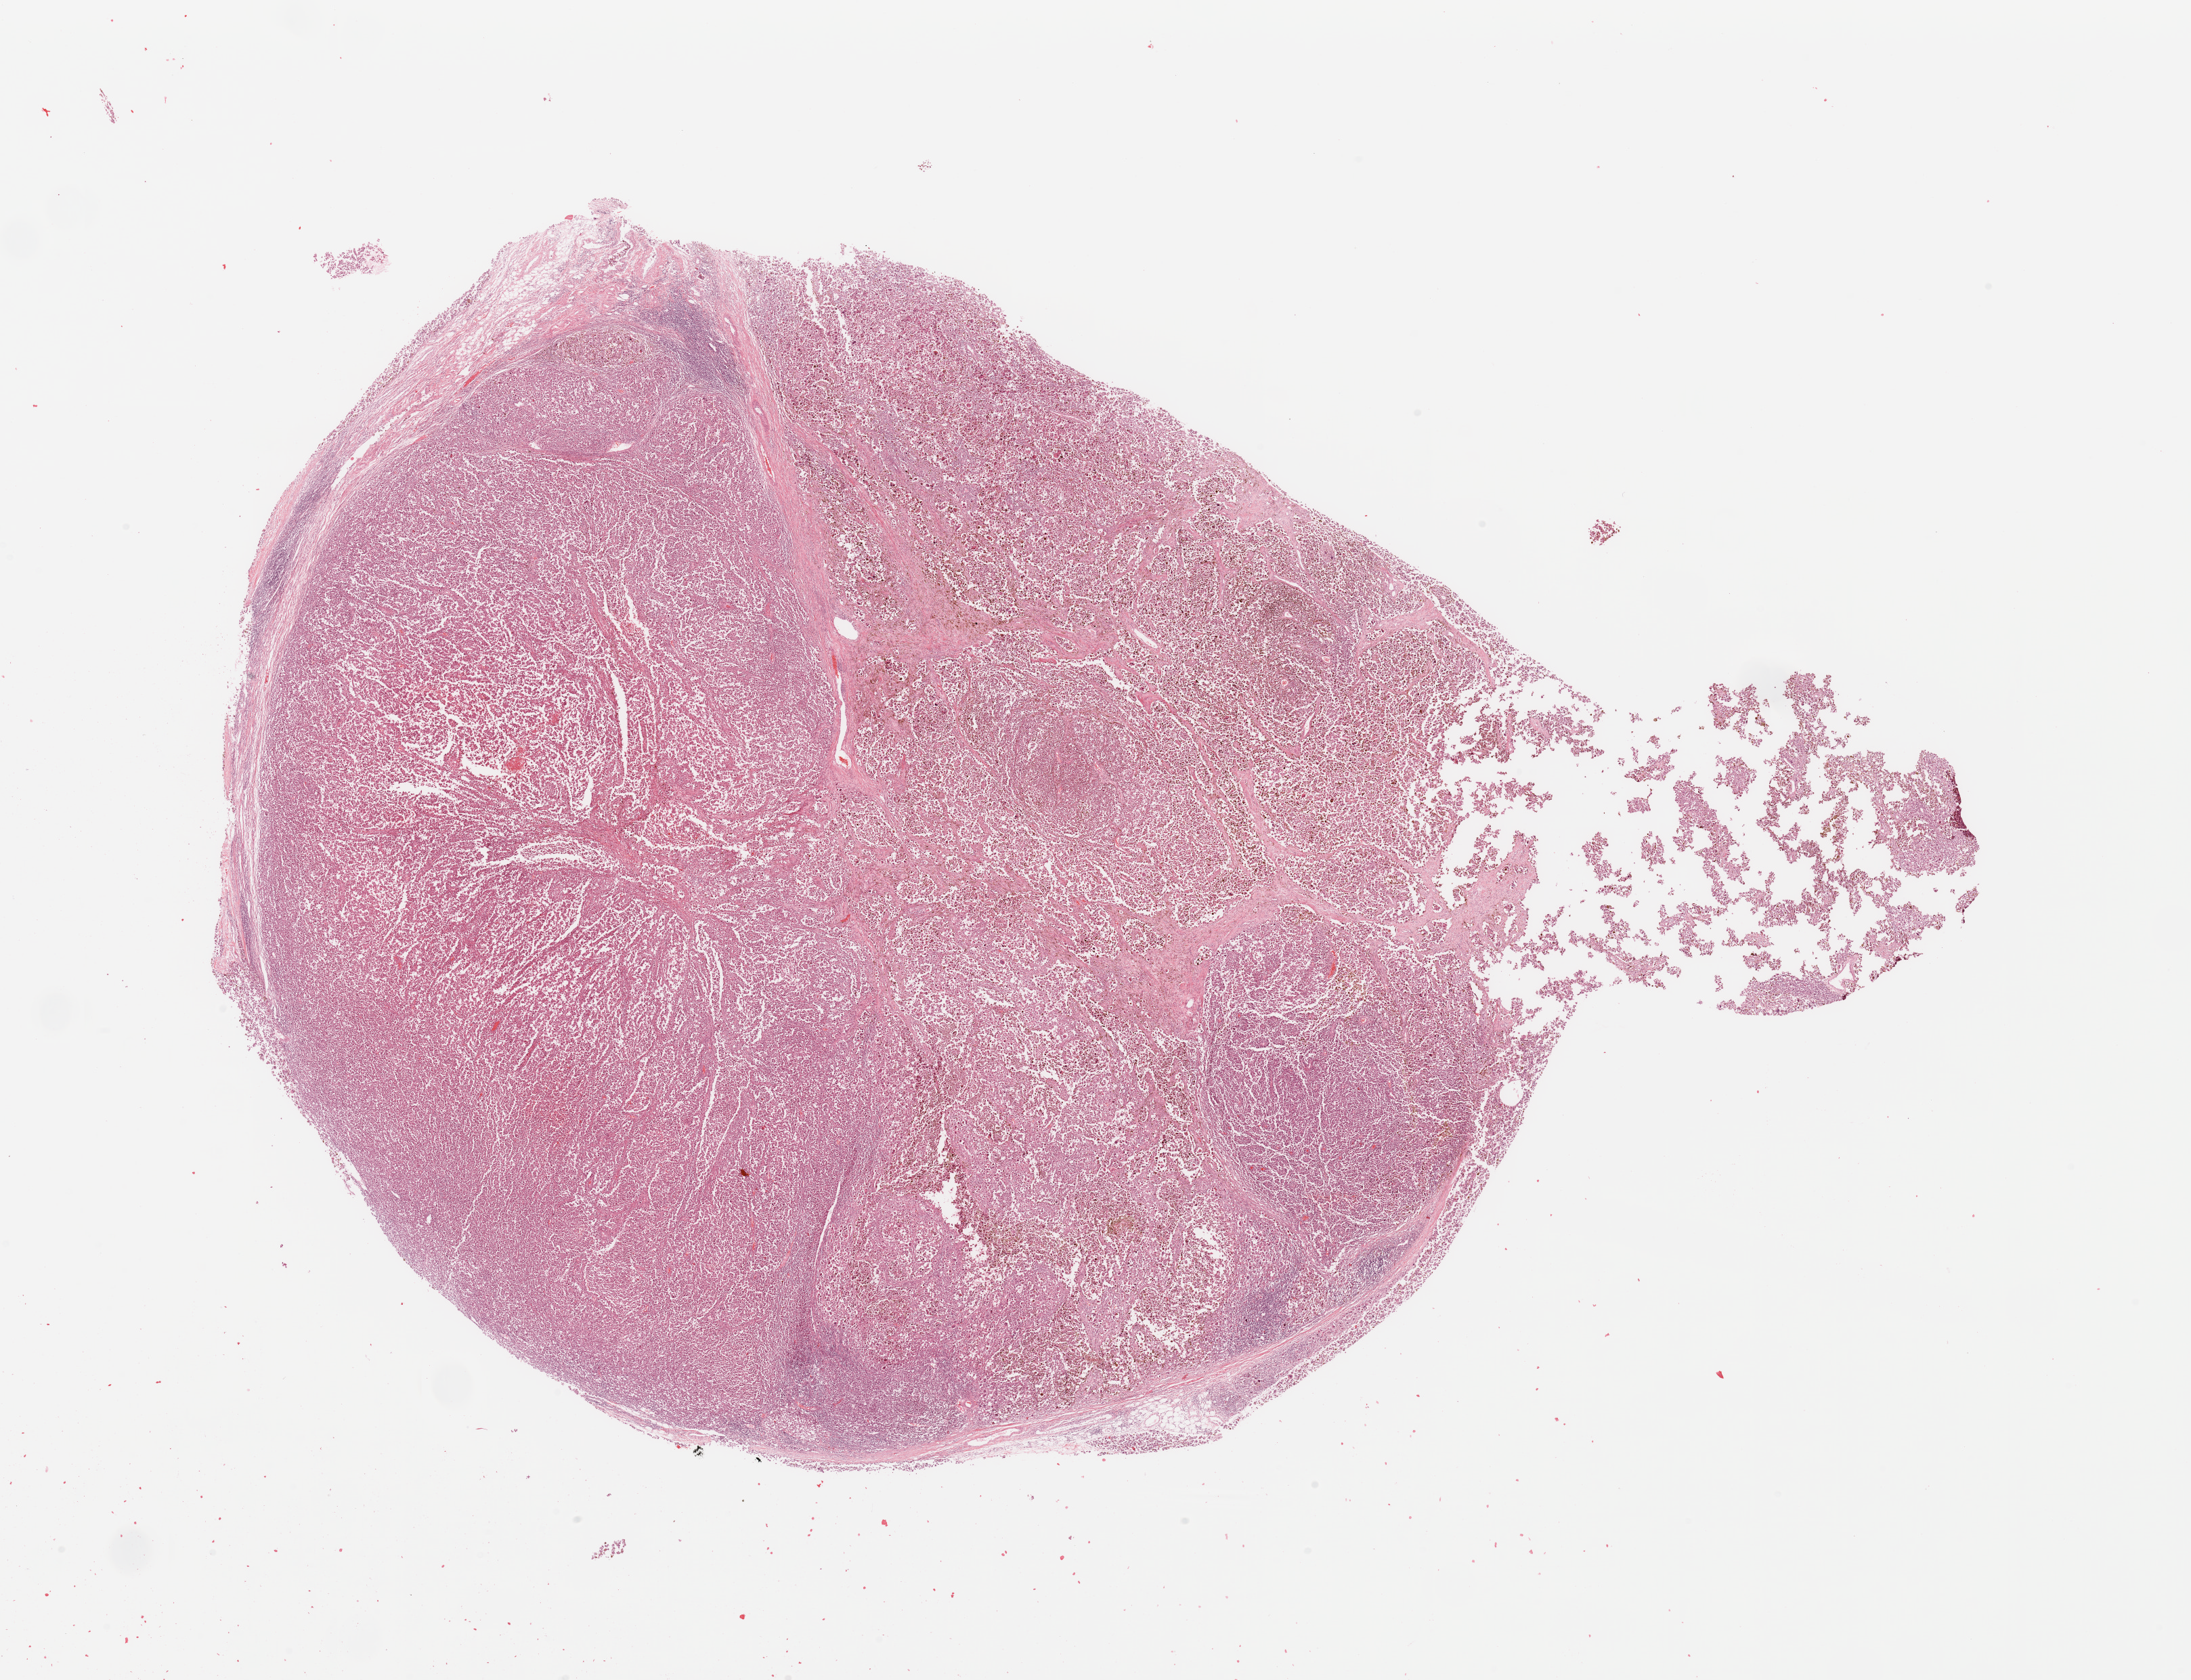
Digitized Hematoxylin and eosin (H&E) stained tissue section (whole slide) — whole scanned area (about 25.6 x 19.6 mm, from a 20x scan) shown as a low-resolution overview; tumour tissue sample, sampled site: lymph node. Patient: male, age 69 years. Composition of this section per pathologist review: tumour nuclei 90%, necrosis 0%.
Diagnosis: Malignant melanoma, NOS. AJCC pathologic stage: IIIC.